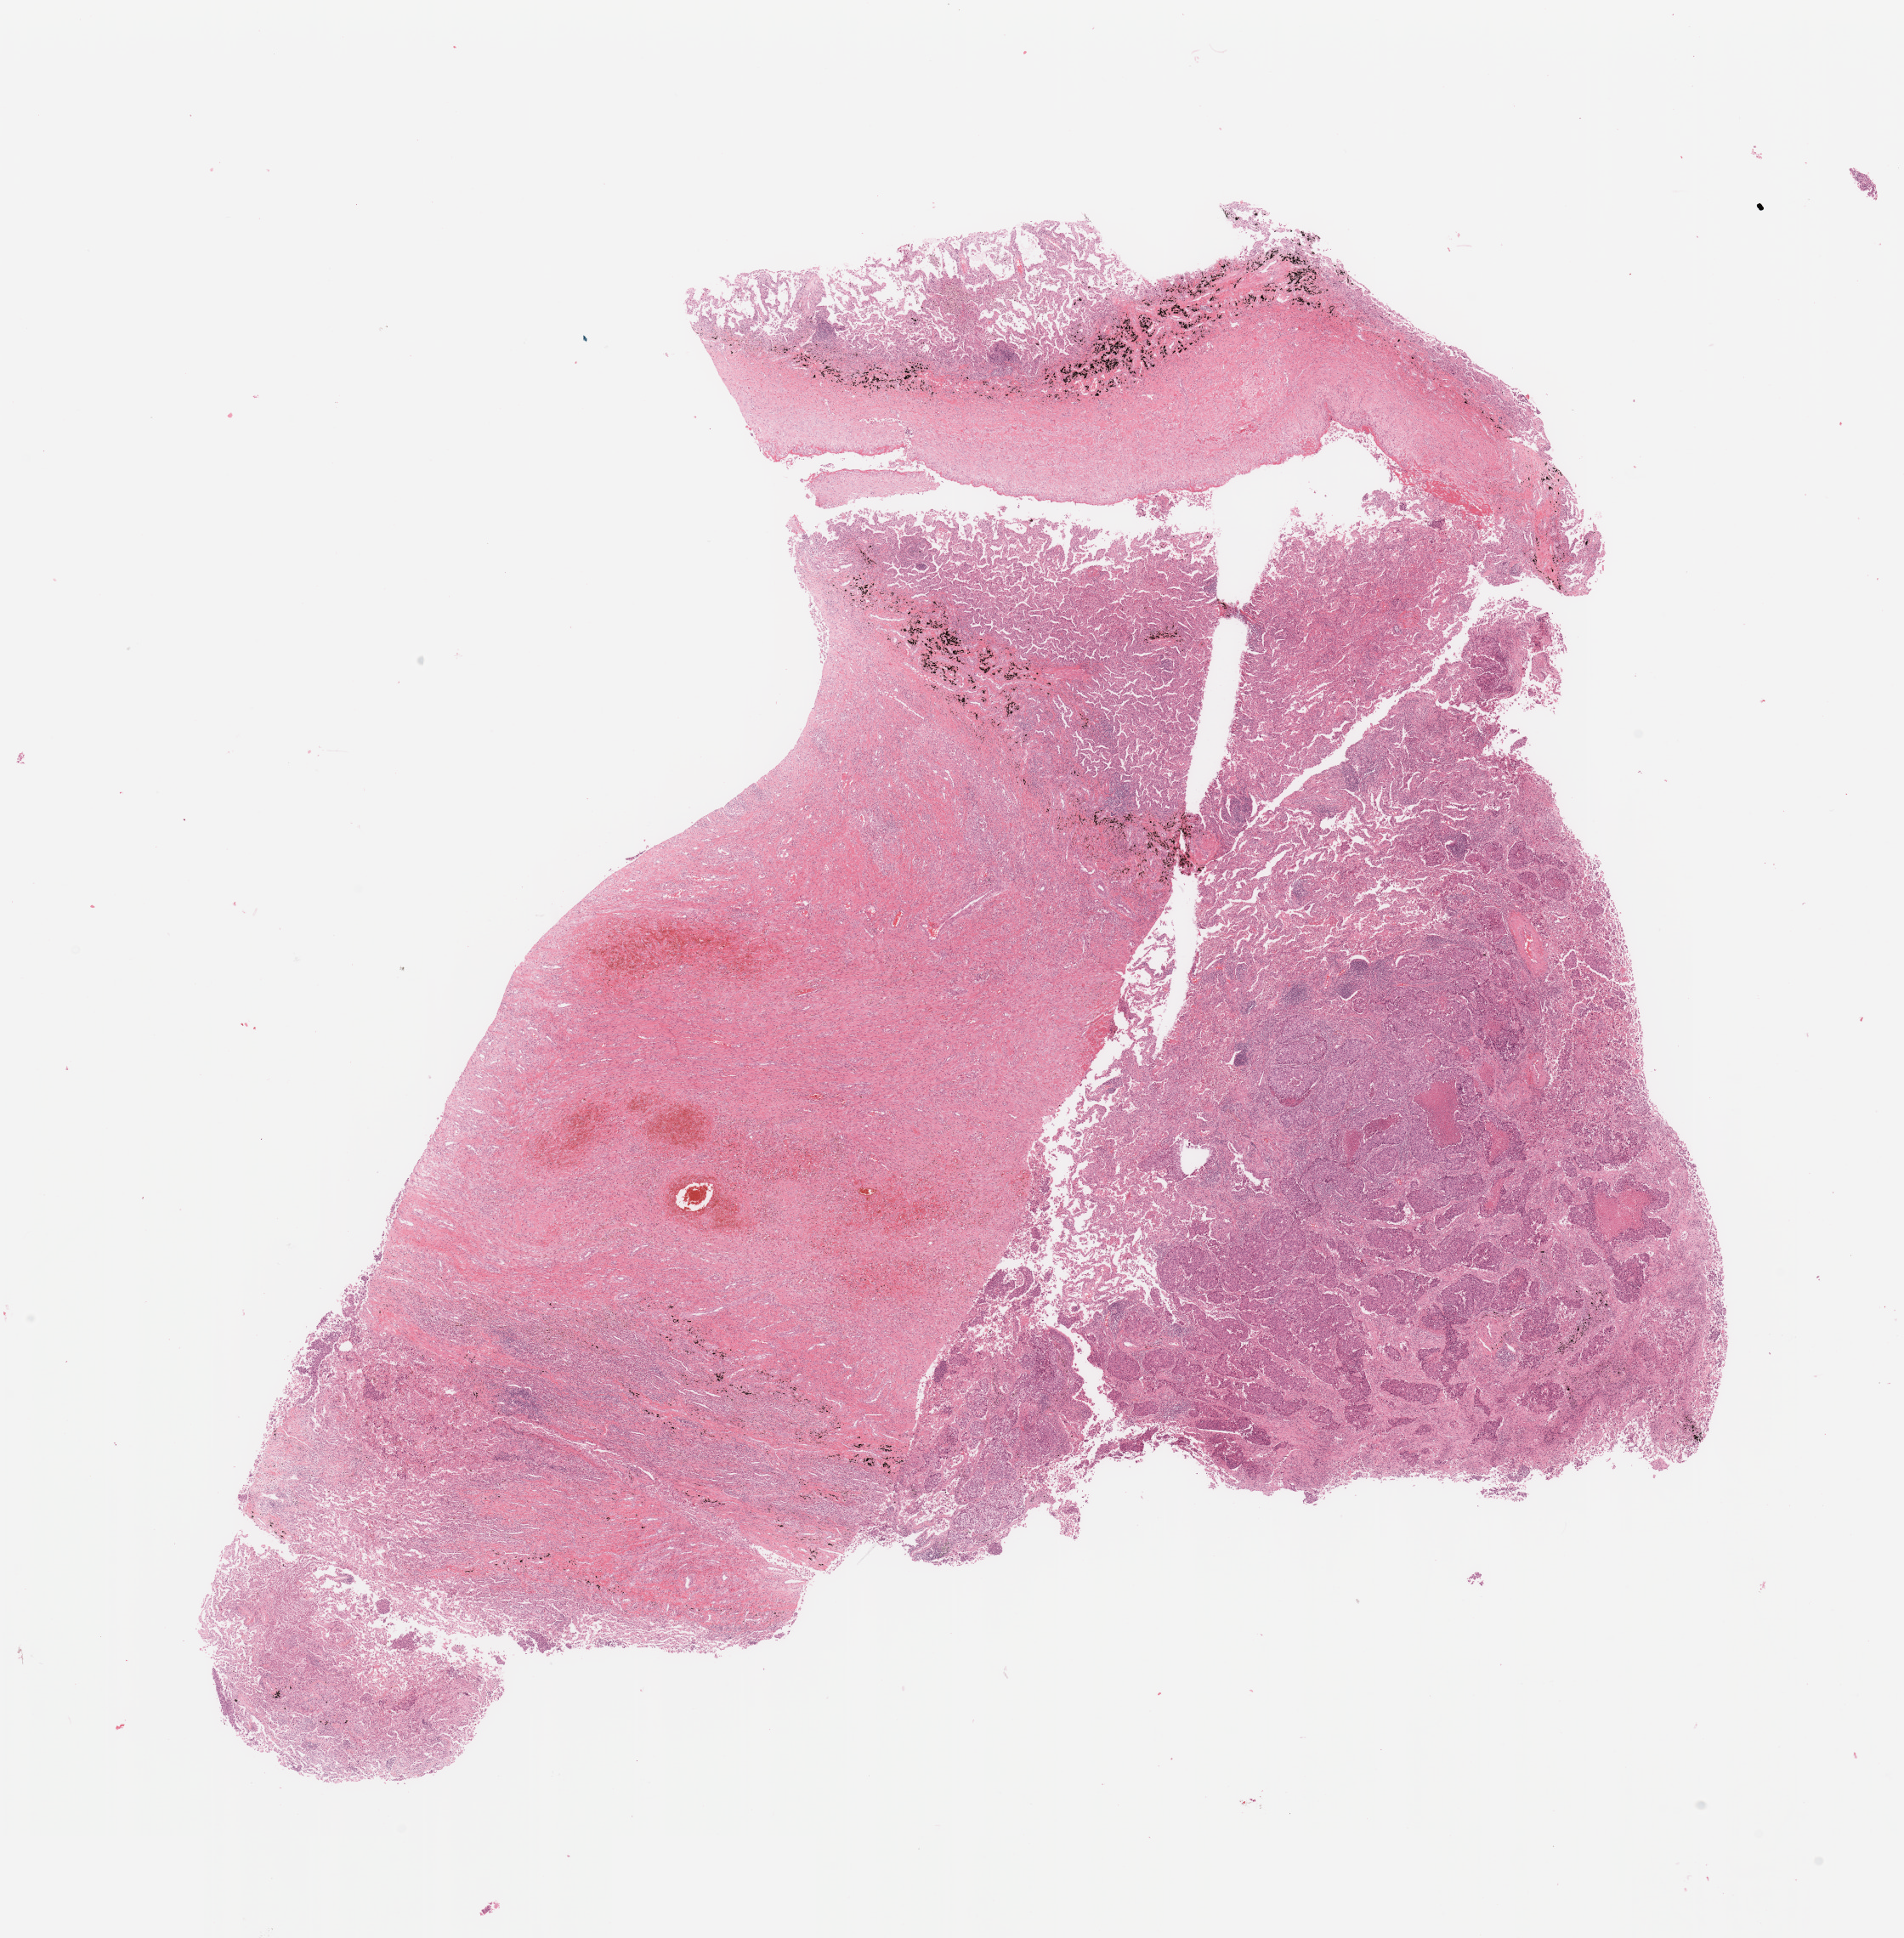
H&E whole-slide image — whole scanned area (about 17.7 x 18.0 mm, from a 20x scan) shown as a low-resolution overview; lung, tumour tissue. Male, 56 y/o. Histologic grade: G3 (poorly differentiated).
AJCC pathologic stage: IB. Primary tumour site (as recorded): left upper lobe. Diagnosis: Adenocarcinoma, NOS.